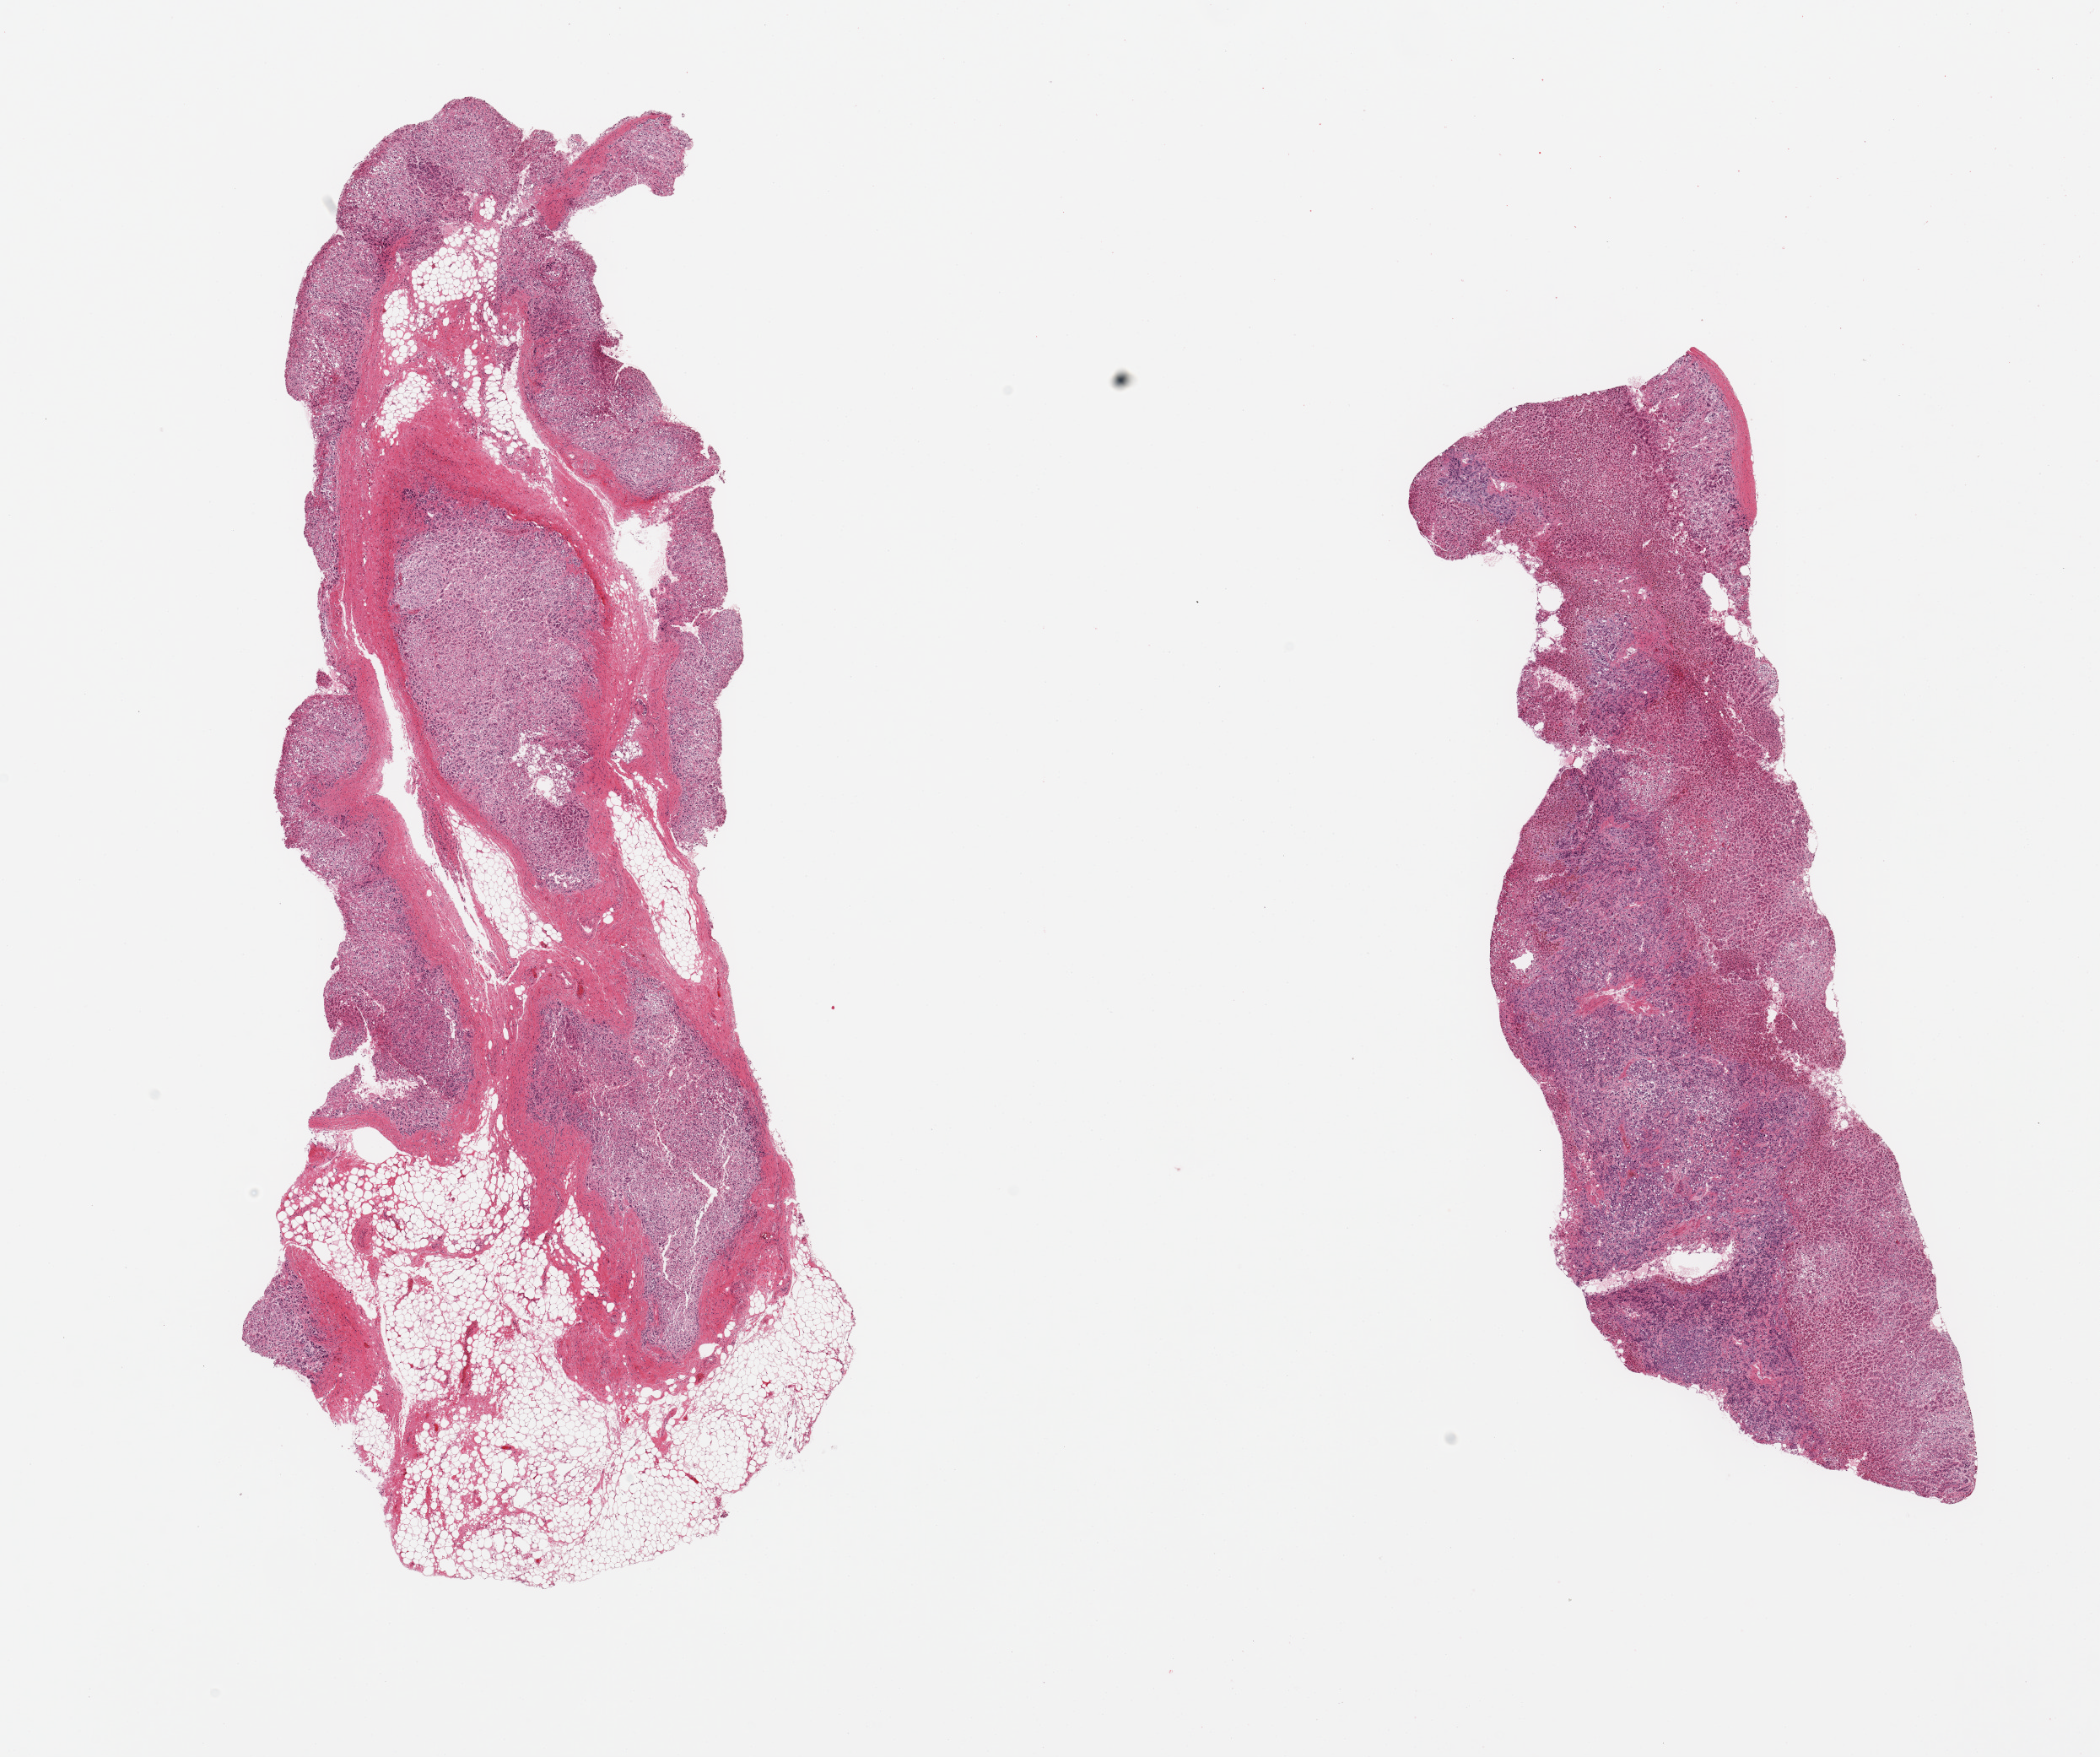
Whole-slide image, hematoxylin and eosin (H&E) stain, low-resolution overview of the scanned area, about 19.7 x 16.5 mm (from a 20x scan), PAXgene-fixed paraffin-embedded (PFPE) section, sampled site (target tissue): adrenal gland, tissue donor sample. Donor: male.
Pathologist's review note for this sample: 2 pieces, cortex, ~20% adherent/interstitial fat.